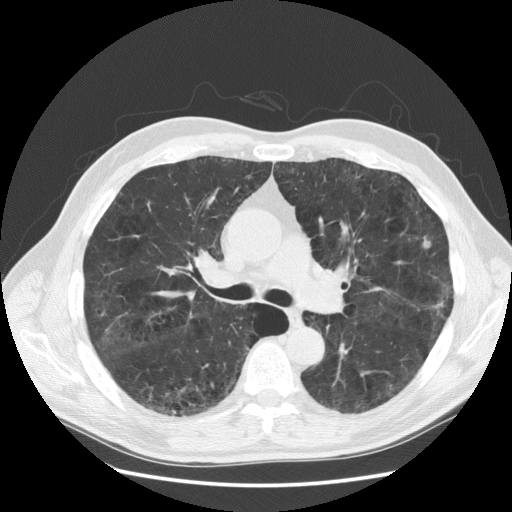
Low-dose screening chest CT, axial slice; third annual screen; lung window (W 1500 / L -600 HU); 2.5 mm slice thickness; standard (soft-tissue) reconstruction kernel (STANDARD). Male participant, aged 58 years at enrolment. Current smoker at enrolment.
• Expert-annotated lung lesion, bounding box [x1, y1, x2, y2] px = [407, 222, 451, 264].
• The exam's reader record, not a measurement of the box and not confirmed to be the same lesion: non-calcified nodule or mass ≥4 mm, left upper lobe, 9 × 8 mm, poorly defined margins, soft tissue attenuation, pre-existing on the prior screen: no.
• Lung cancer was diagnosed 53 days after this screen: adenocarcinoma, NOS, left upper lobe, stage IA (AJCC 6th edition), 9 mm at pathology.